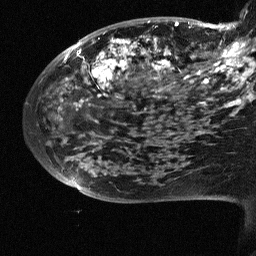
Breast MRI (dynamic contrast-enhanced), one sagittal slice. Slice 20 of 64 in the series (ordered by position). Dynamic contrast-enhanced study with each time point stored as its own series, time point 2 of 3 at this slice position (early post-contrast, ordered by acquisition time). 1.5 T. TE 4.5 ms, TR 11 ms. 2.5 mm slice thickness. 256 × 256 image matrix, field of view 200 × 200 mm. Female patient, age 38 years. From the clinical record (not read from this slice): setting: breast cancer imaged before/during neoadjuvant chemotherapy; receptor status: HR-positive, HER2-negative.
Structures marked on this image (semi-automatic segmentation, software-assisted and operator-edited):
- analysis volume of interest (the breast-tissue region the enhancement analysis was run in; not a lesion): box from (x=88, y=18) to (x=252, y=126) px
- tumour enhancement mask (voxels above the 90 % enhancement threshold inside the analysis volume of interest): (x=90, y=22)–(x=252, y=107)